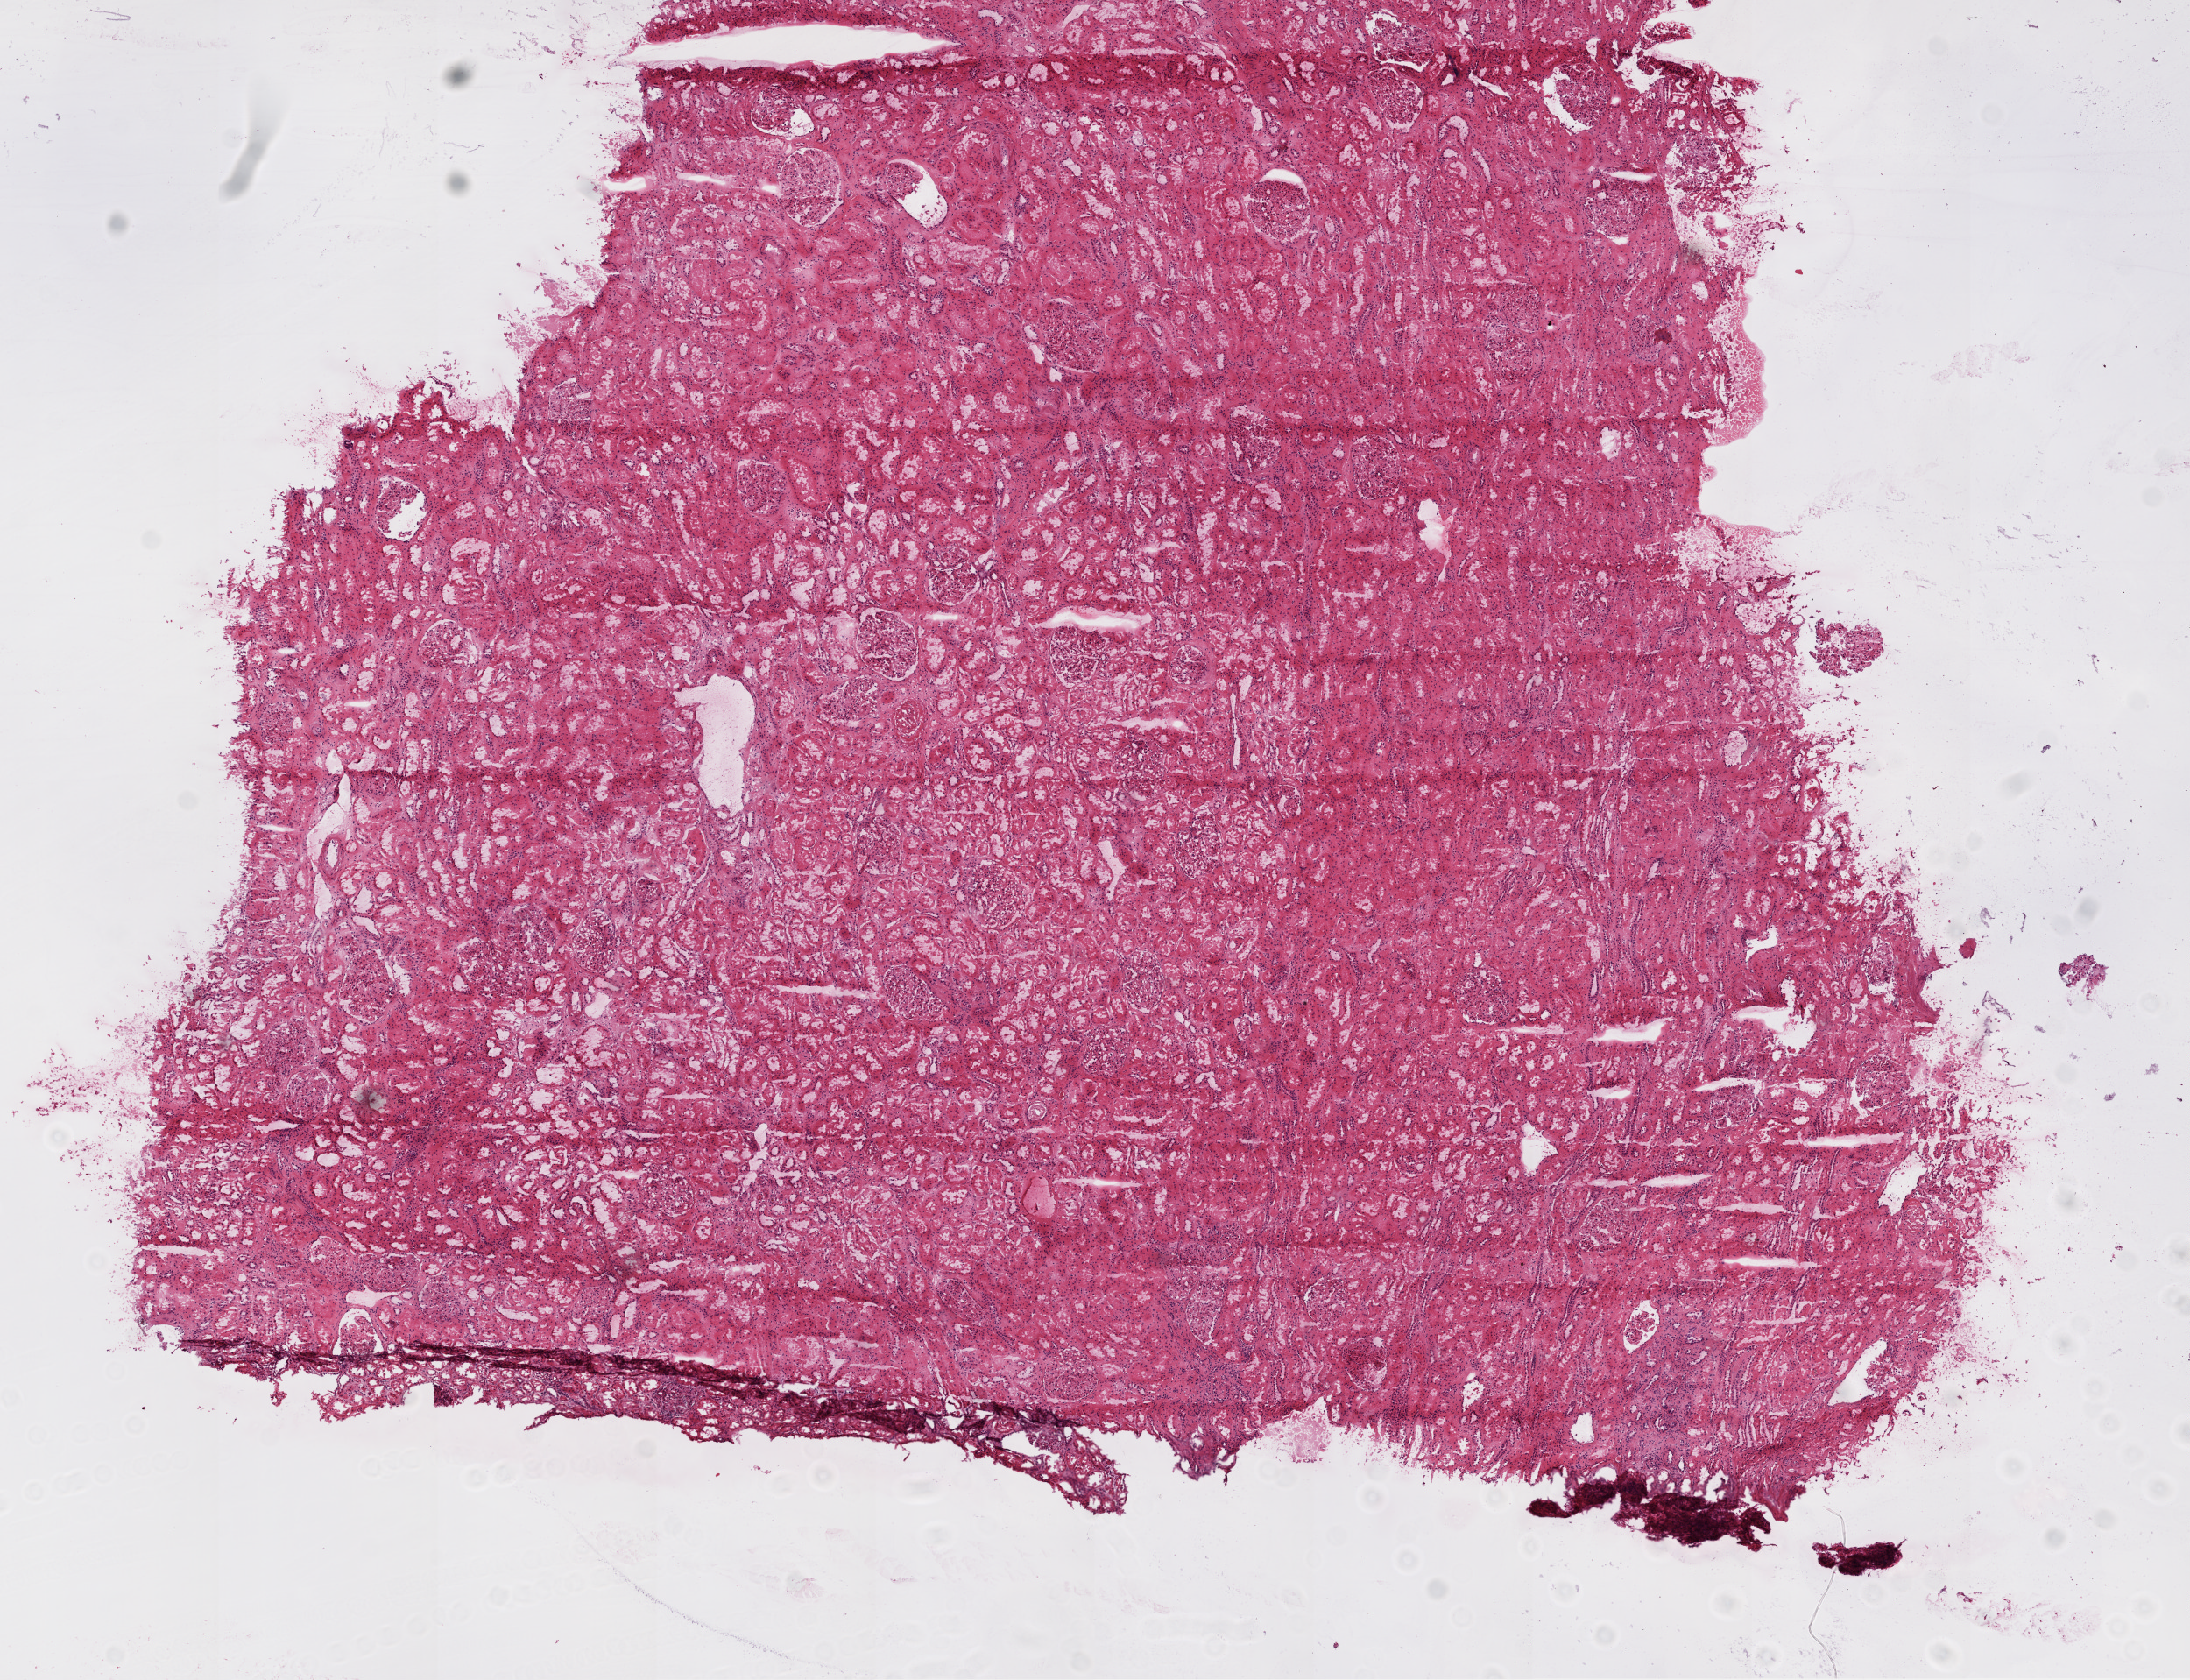
Digitized Hematoxylin and eosin (H&E) stained tissue section (whole slide), low-resolution overview of the scanned area, about 10.0 x 7.7 mm, frozen section from the top of the tissue portion, sample: solid tissue normal (non-tumour tissue), kidney. Male patient; age at initial diagnosis 57 years.
This section: solid tissue normal sample (biorepository sample class). Patient diagnosis: Clear cell adenocarcinoma, NOS.